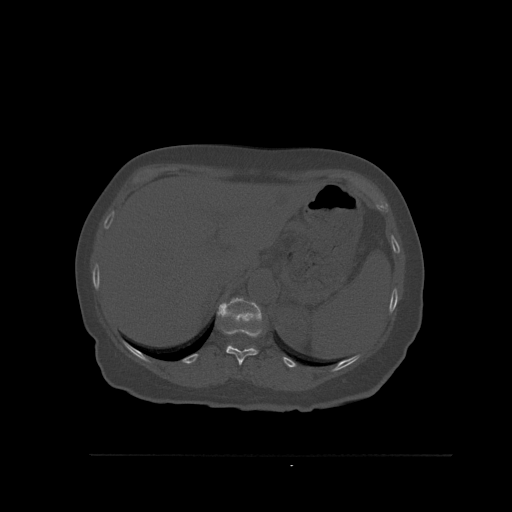
CT including the spine, one axial slice. Position 299 of 527 along the scan axis. Bone window (W 1800 / L 400 HU). 1.5 mm slice thickness. 512 × 512 image matrix, field of view 470 × 470 mm. Patient: female, 73 years. From the clinical record (not read from this slice): primary cancer: breast; vertebrae with lytic lesions (as recorded): L2.
Structures marked on this image (semi-automatically segmented with operator editing):
- T11 vertebra: bounding box [x1, y1, x2, y2] px = [222, 327, 262, 365]
- T12 vertebra: [217, 297, 262, 346]